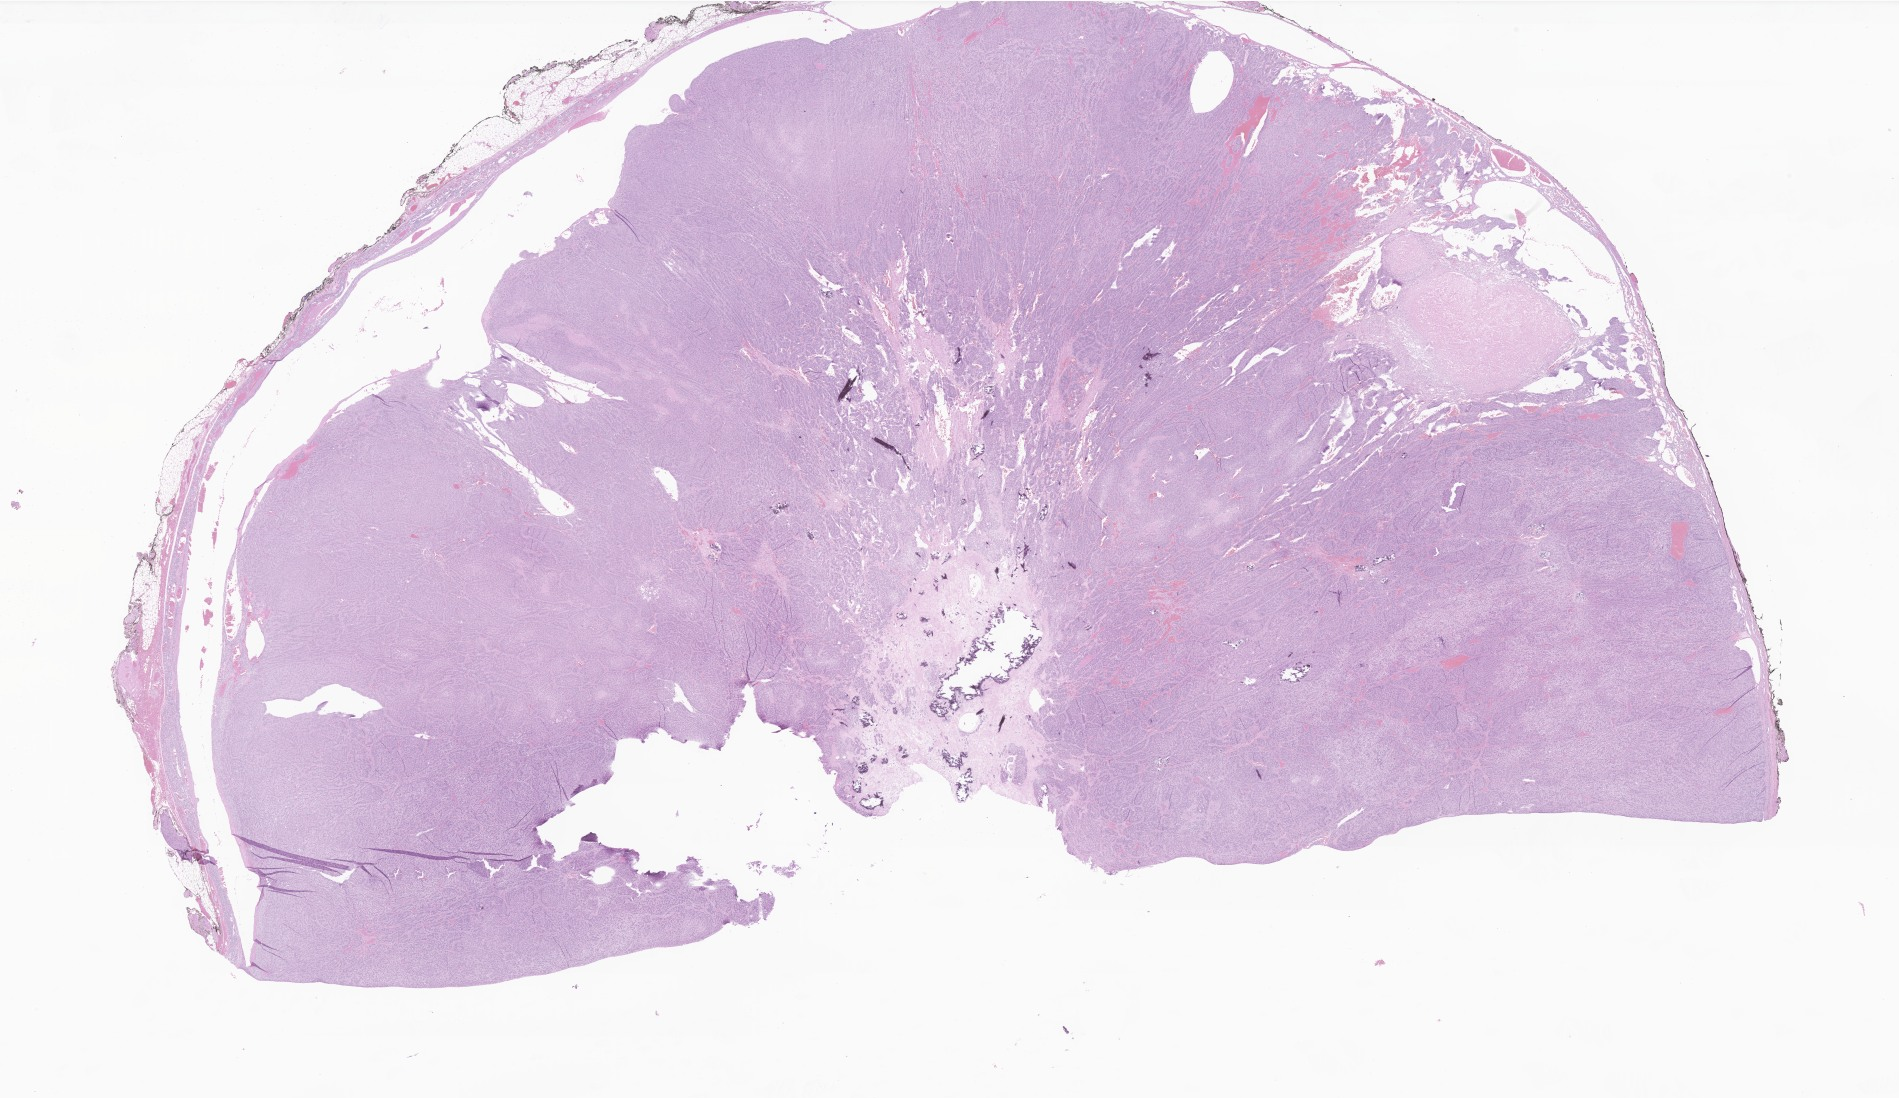
Whole-slide image, H&E stain of tumor tissue from the adrenal gland — whole scanned area (about 32.0 x 18.5 mm) shown as a low-resolution overview; FFPE section. Patient: female, age 94 months (7 years 10 months).
- diagnosis (ICD-O-3 morphology term): Adrenal cortical carcinoma